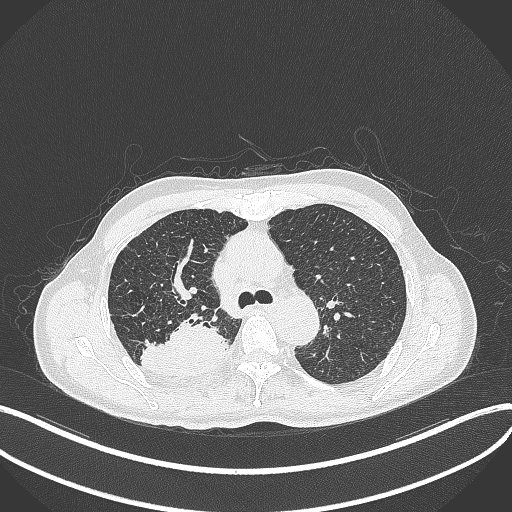
Chest CT, one axial slice; position 311 of 428 along the scan axis; reconstruction kernel B70f; lung window (W 1500 / L -600 HU); 1 mm slice thickness; 512 × 512 image matrix. Male patient, age 79 years. Case-level facts recorded for this patient, not image findings: clinical TNM (as recorded): T3 N0 M0.
Outlined on this slice (rectangle marked by the reading radiologist):
- lung tumour (recorded histology: adenocarcinoma): bounding box (x1, y1, x2, y2) in pixels: (140, 310, 228, 379)